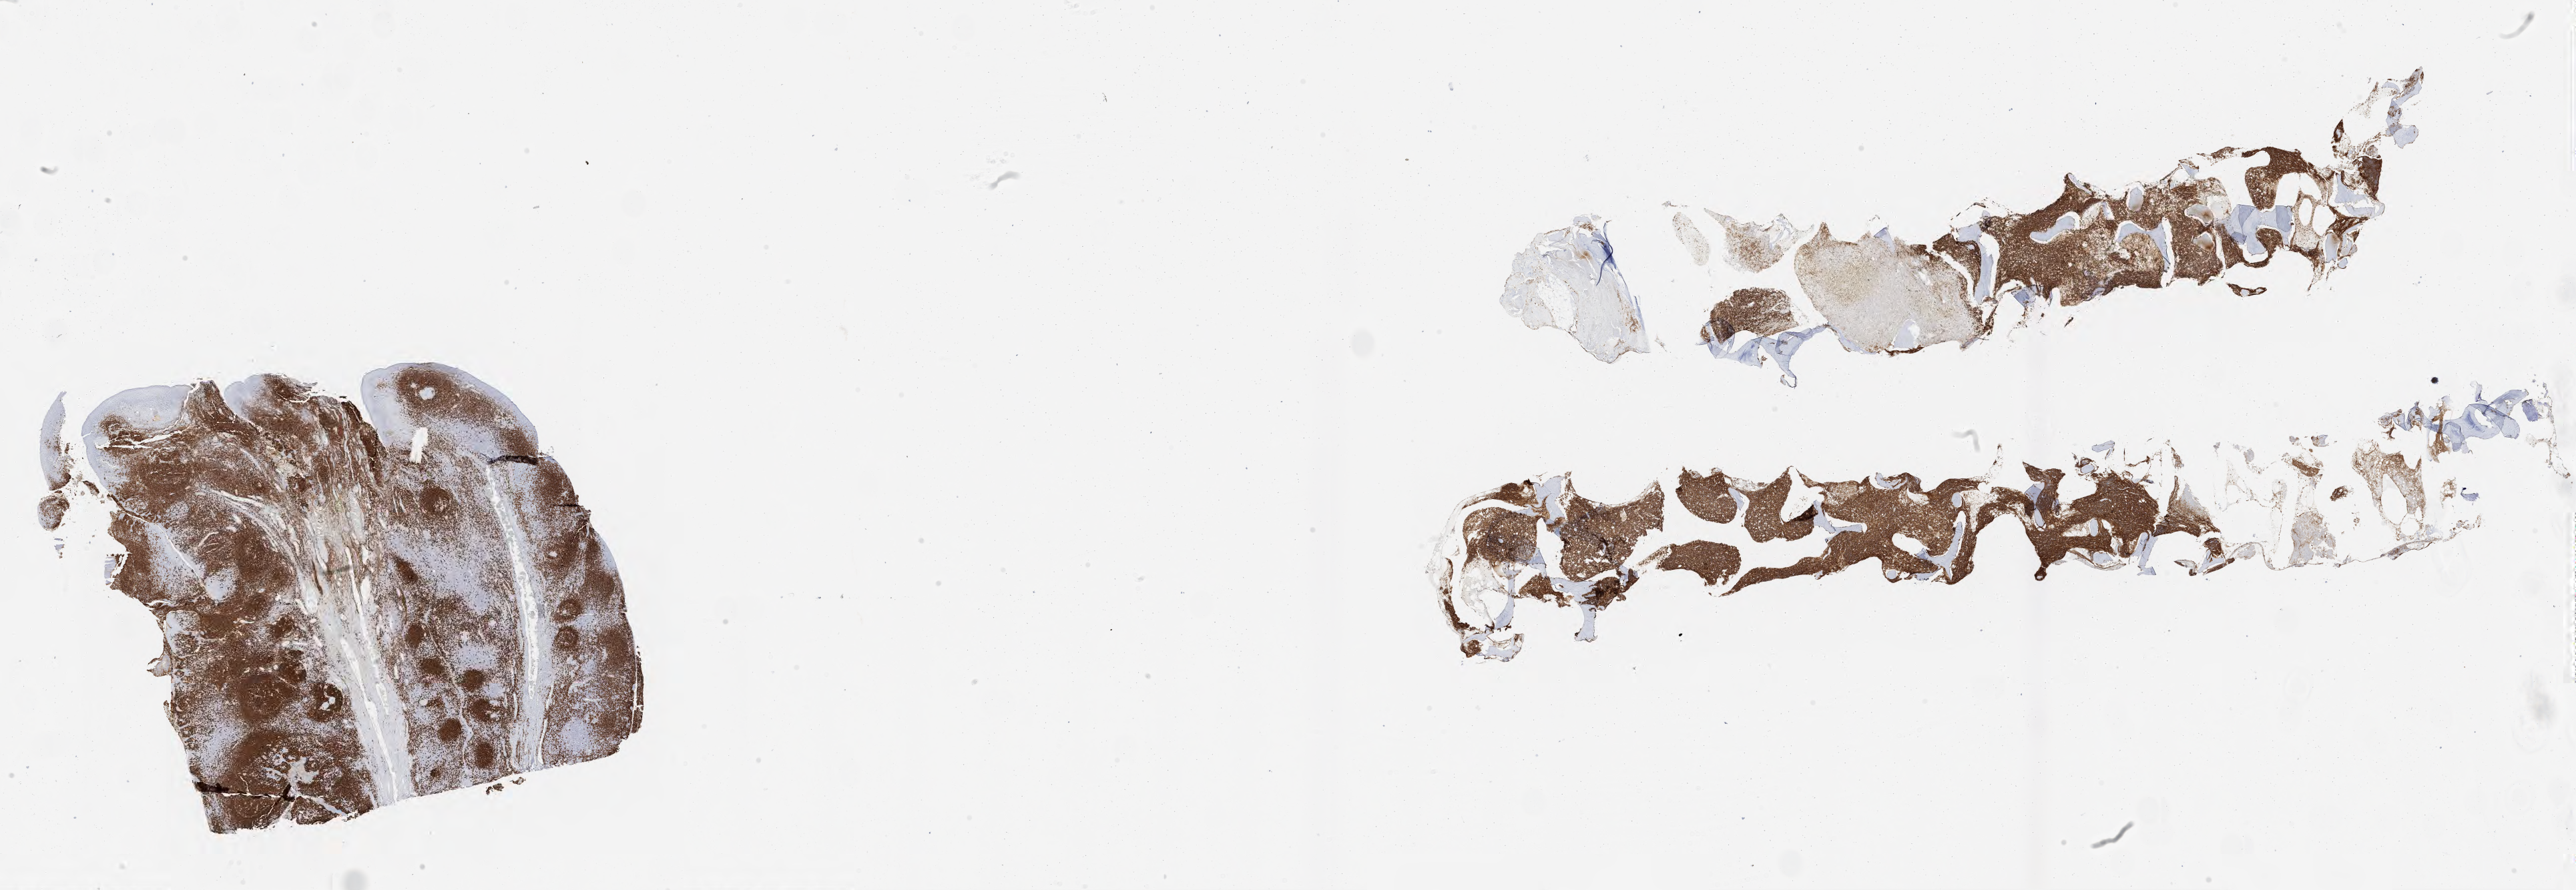
Immunohistochemistry (IHC) whole-slide image stained for CD20 — low-resolution overview of the scanned area, about 31.0 x 10.7 mm; tumor tissue. Patient female; 60 years old.
- diagnosis: Burkitt lymphoma, NOS